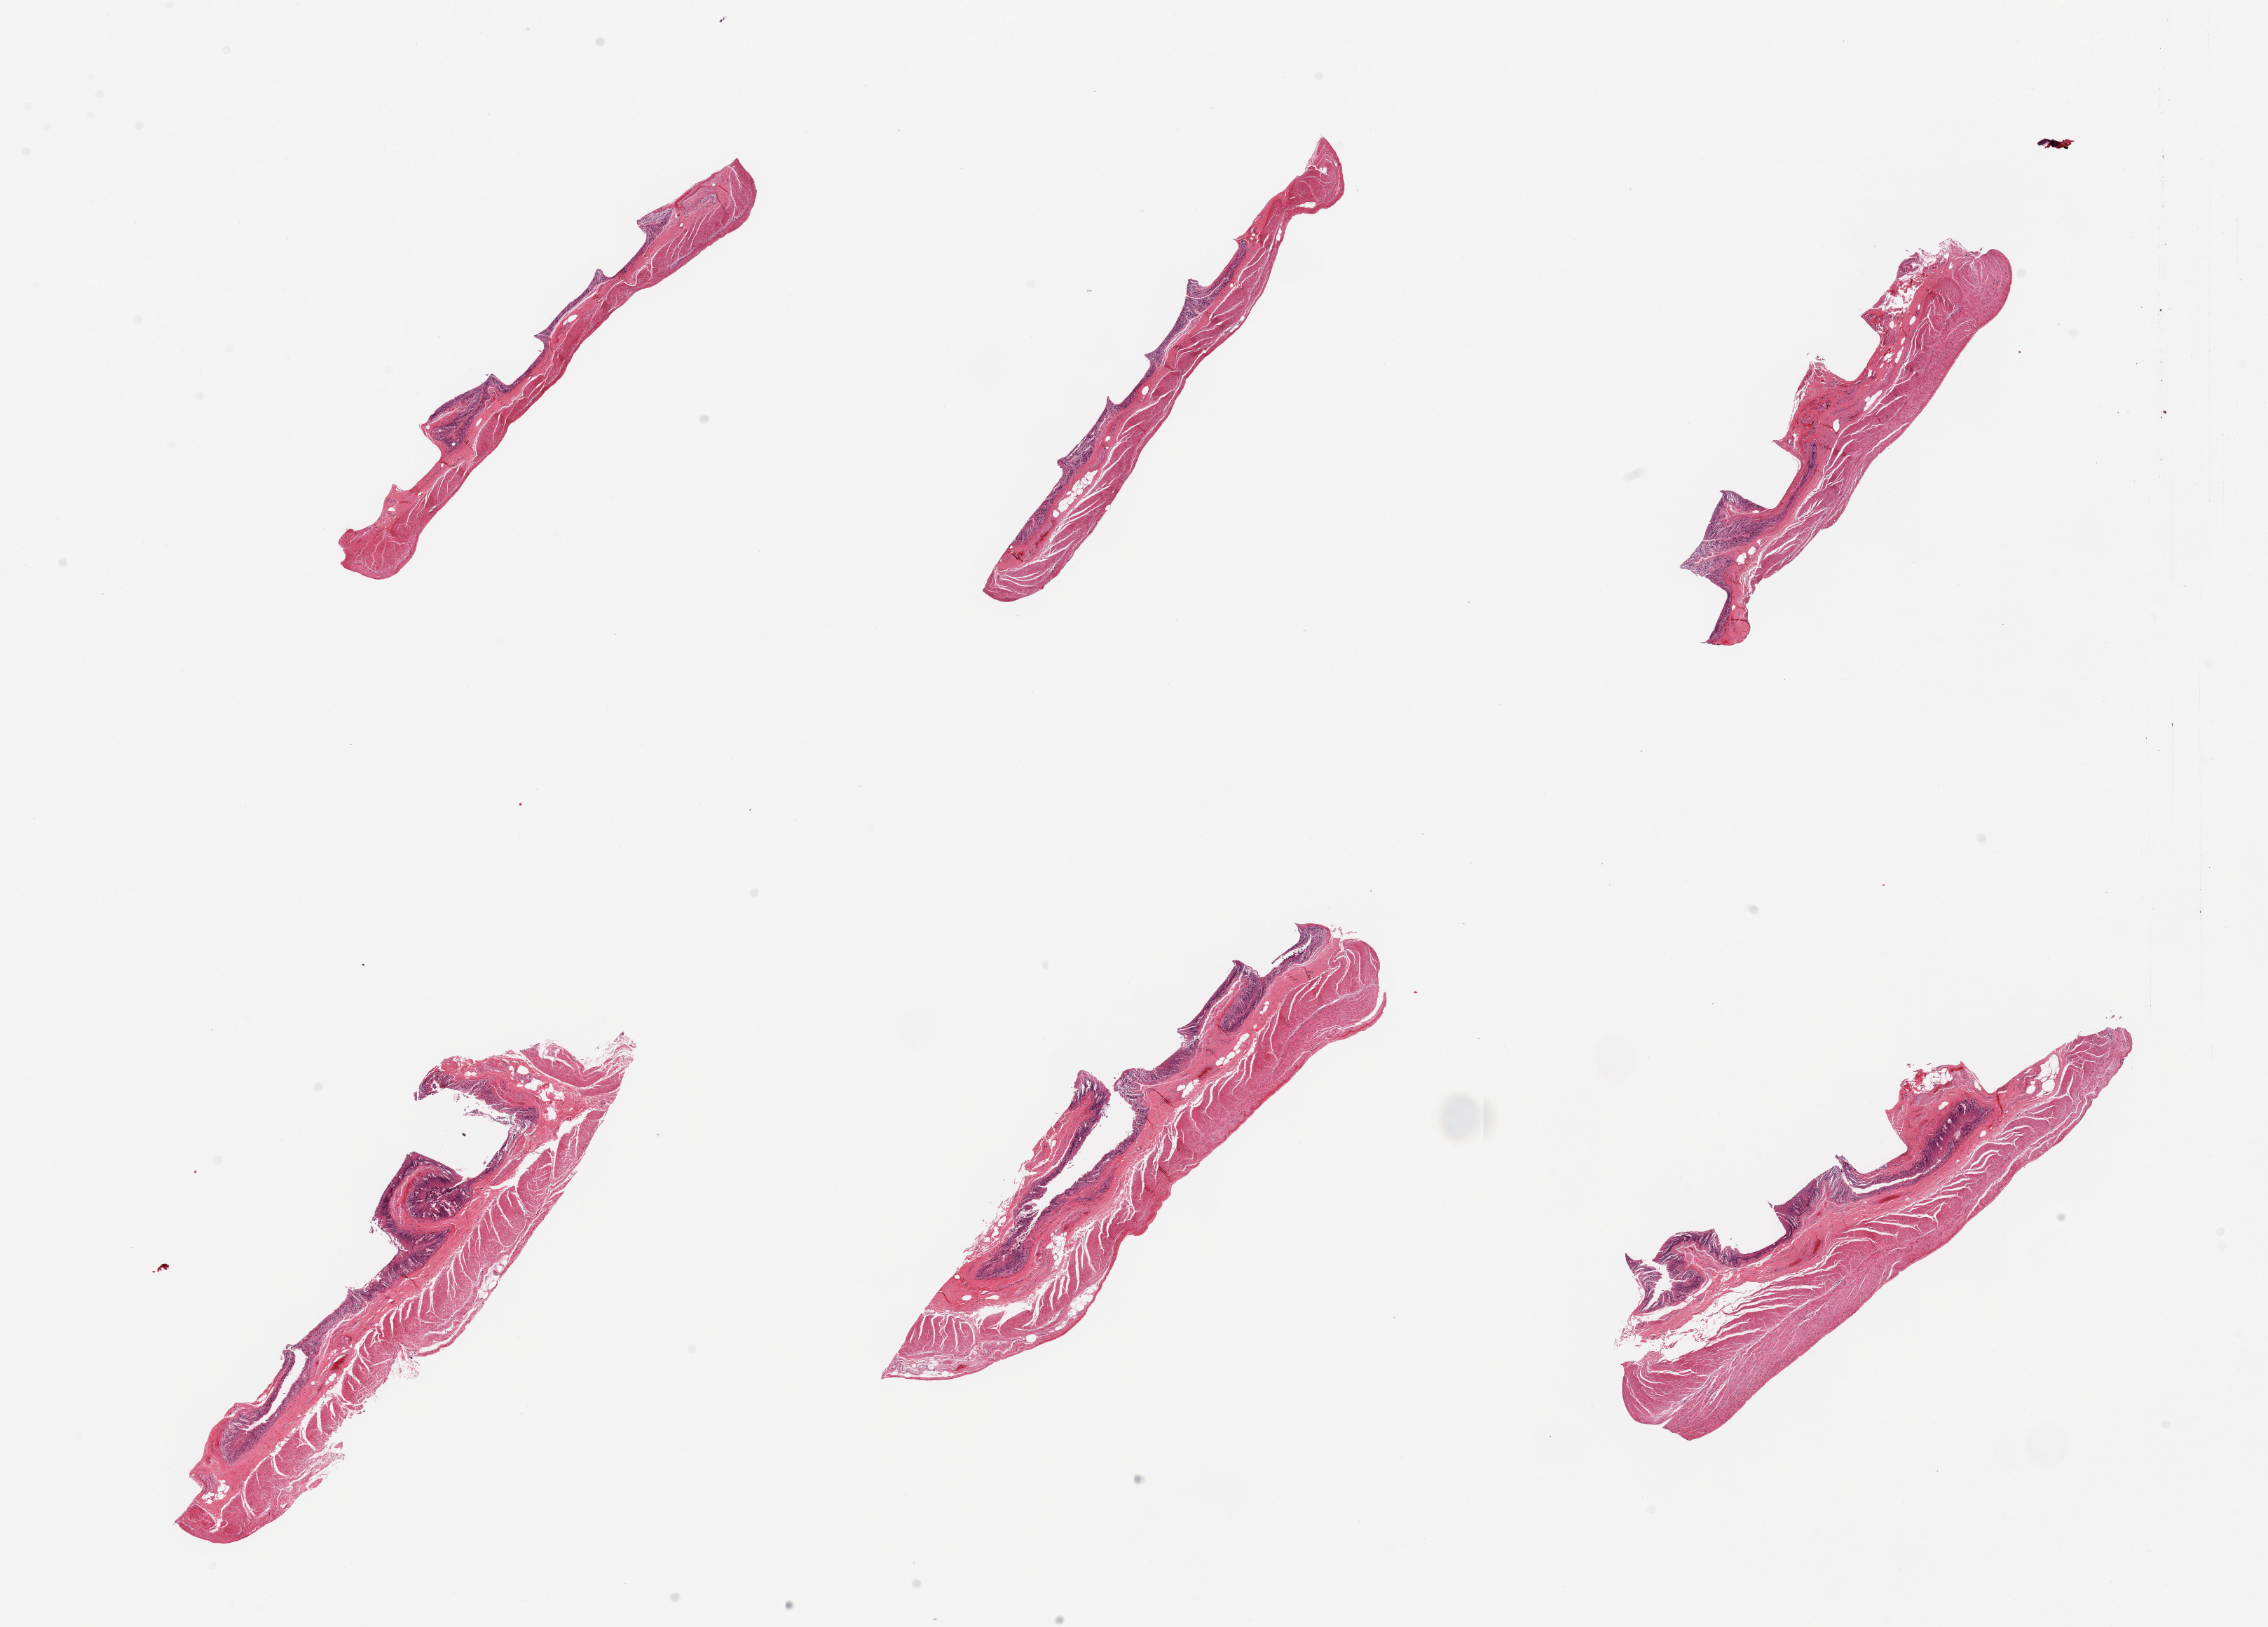
Whole-slide image, hematoxylin and eosin (H&E) stain, brightfield, whole scanned area (about 25.6 x 18.4 mm, from a 20x scan) shown as a low-resolution overview; PAXgene-fixed, paraffin-embedded tissue; section of transverse colon (target tissue); donor tissue sample.
Review note (as recorded): 6 pieces, mucosal glandular elements totally sloughed, up to ~0.3mm thick.